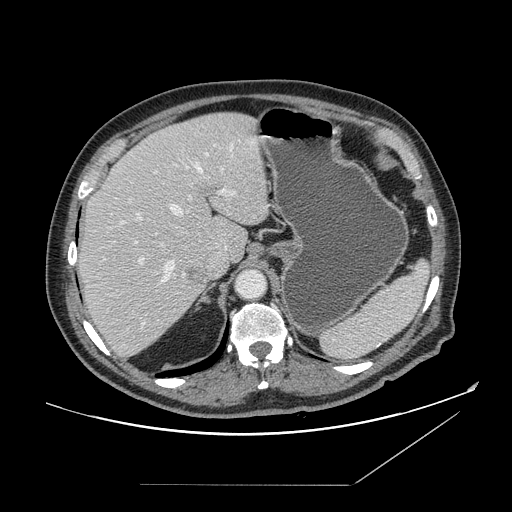
Contrast-enhanced abdominal CT, one axial slice. Slice 113 of 166 in the series (ordered by position). 120 kVp. Intravenous contrast given. Soft-tissue window (W 400 / L 40 HU). 2.5 mm slice thickness. 512 × 512 image matrix. Male patient, age 80 years. From the clinical record (not read from this slice): diagnosis: colorectal cancer liver metastases, imaged before liver resection; multiple liver metastases: no; largest metastasis: 2.2 cm; chemotherapy before resection: no.
Outlined on this slice (outlined manually by an expert reader):
- hepatic veins: bounding box [x1, y1, x2, y2] px = [137, 144, 233, 284]
- liver: [78, 113, 270, 357]
- planned liver remnant (the part of the liver to remain after resection): [84, 113, 269, 261]
- portal vein (with intrahepatic branches): [130, 154, 233, 325]
- liver metastasis: [189, 269, 198, 277]
- liver metastasis: [186, 269, 204, 283]